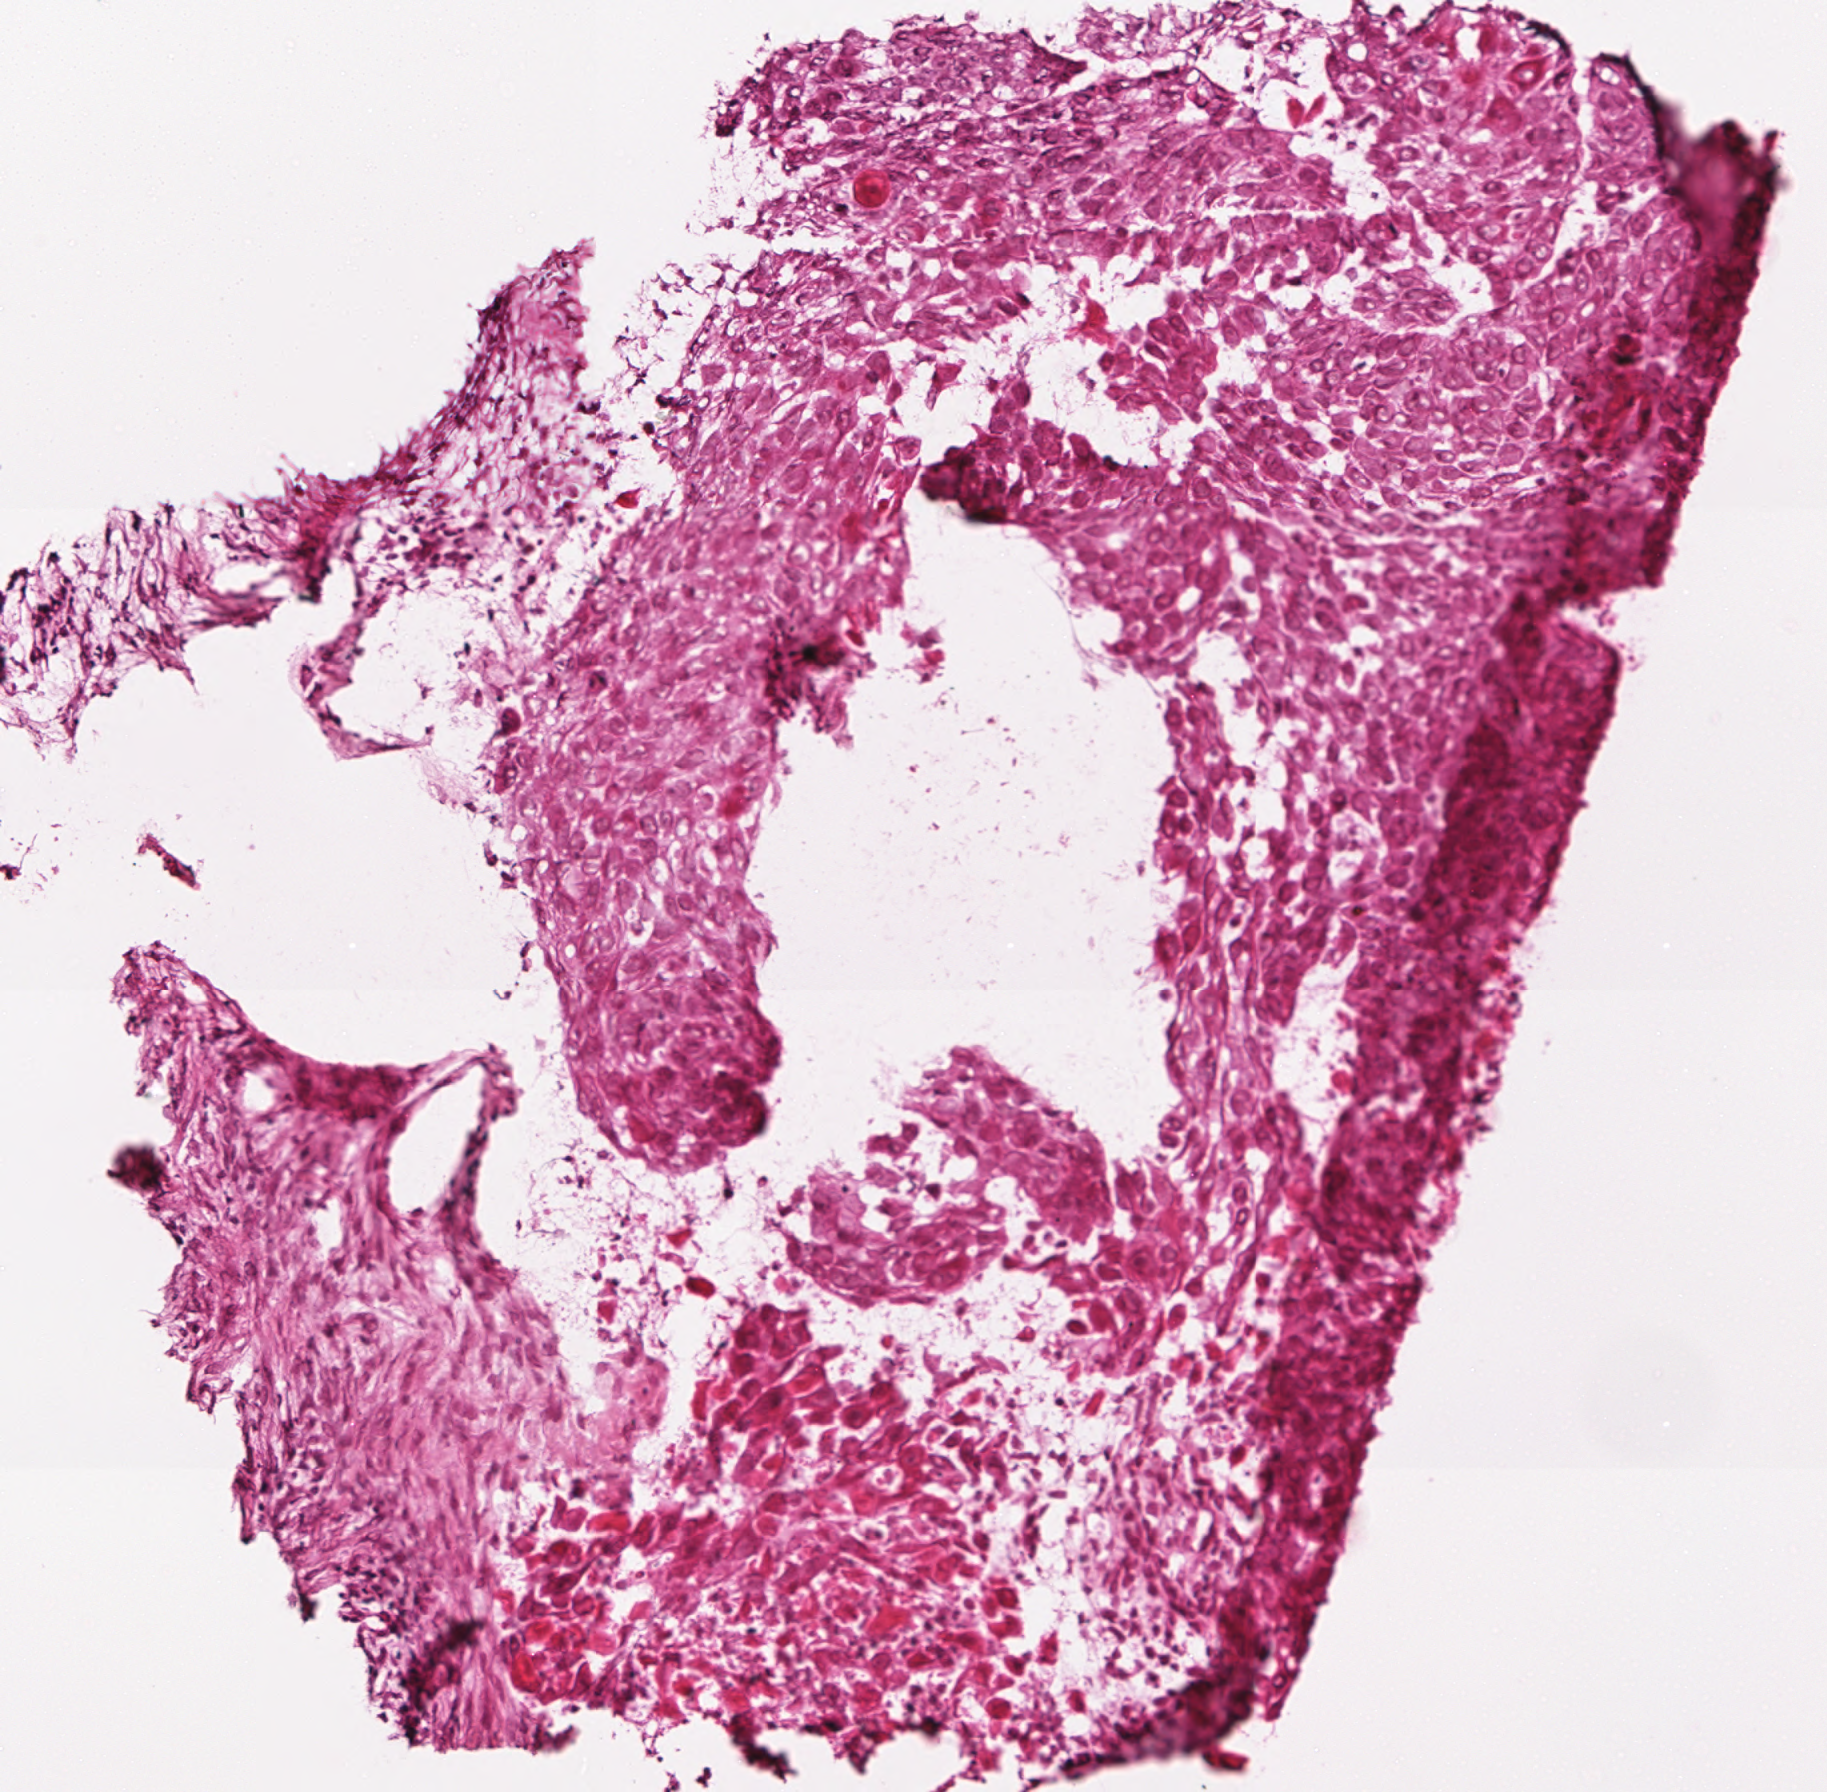
Whole-slide histology image, H&E — low-resolution overview of the scanned area, about 1.8 x 1.8 mm; frozen section; head and neck, primary tumour sample. Male patient; age at initial diagnosis 44 years. Histologic grade: G2 (moderately differentiated). Pathologist review of this section (percent, as recorded): tumour cells 100%, tumour nuclei 90%, normal cells 0%, stromal cells 0%, necrosis 0%. Inflammatory infiltration, as recorded: lymphocyte infiltration 5%, monocyte infiltration 0%, neutrophil infiltration 0%.
AJCC pathologic stage: IVA (7th edition). TNM: T3 N2b M0. Diagnosis: Squamous cell carcinoma, NOS (tongue, NOS).